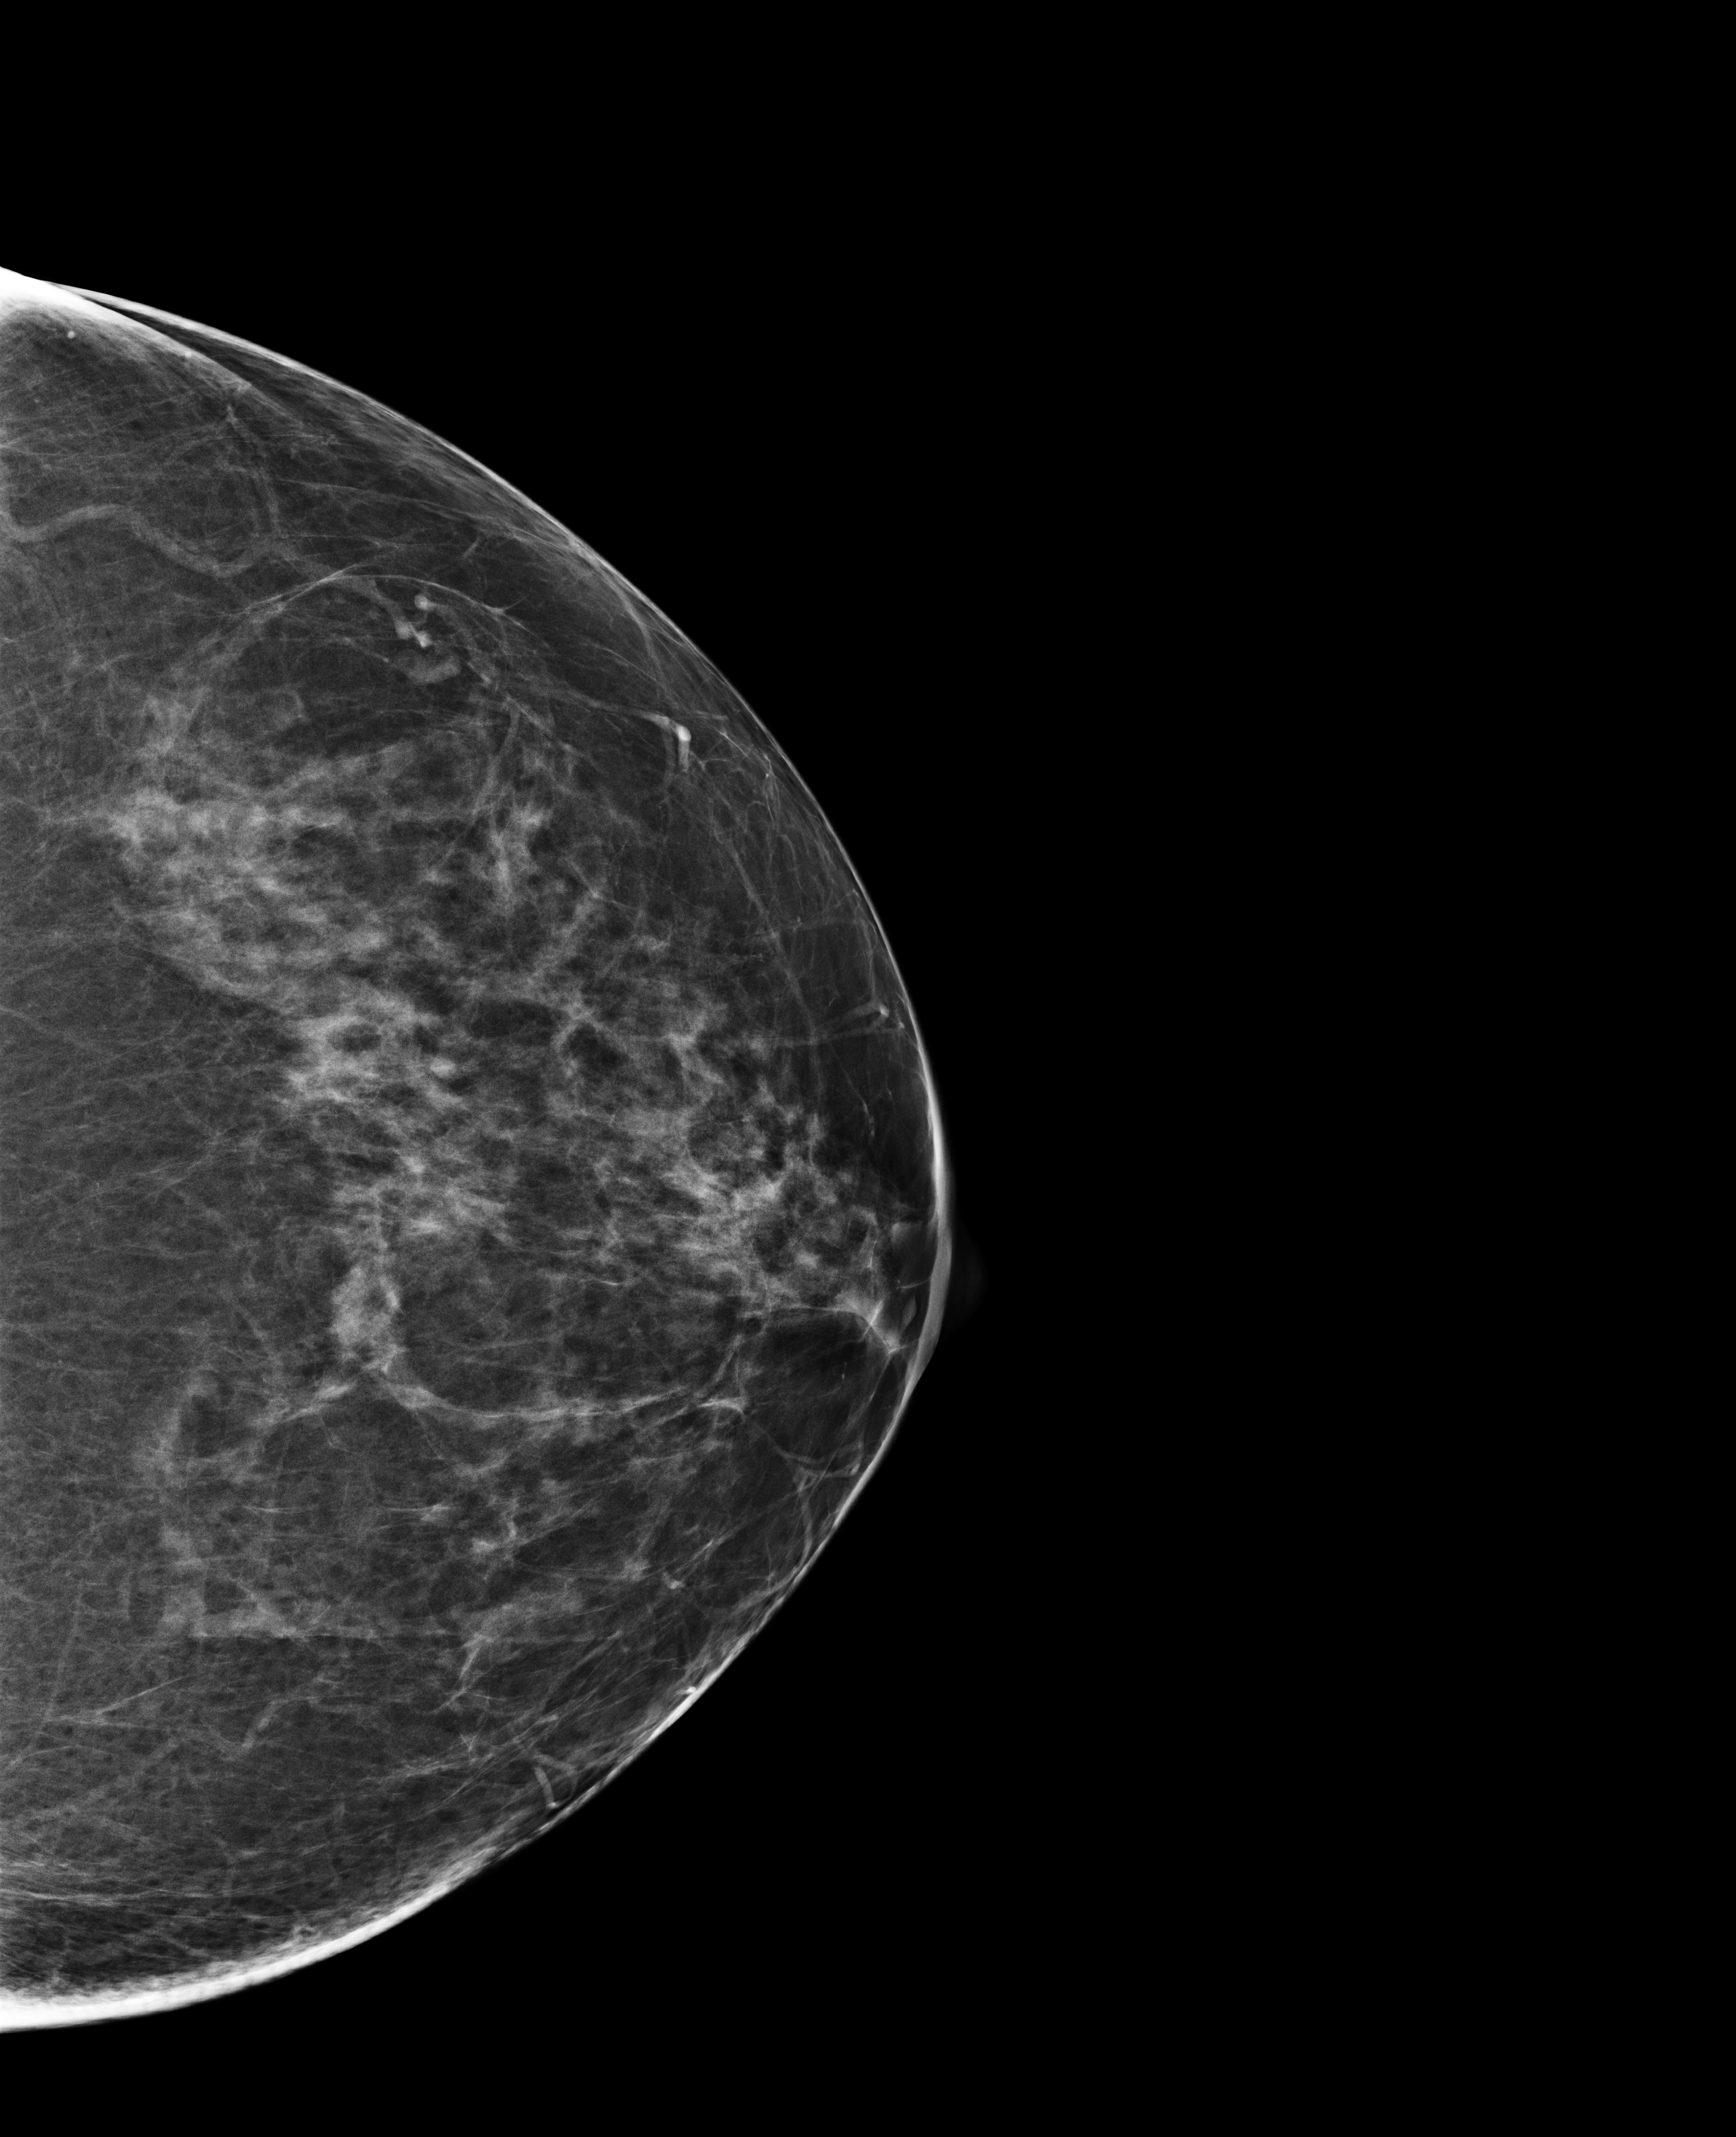
Digital mammogram (FFDM); left breast; craniocaudal (CC) view; annual screening mammography examination; compressed breast thickness 84 mm; system: Selenia Dimensions. Patient: female, 59 years.
BI-RADS breast density category at the screening exam (both breasts, scale 1–4): 3. Final BI-RADS assessment for this screening round (tomosynthesis exam, both breasts): category 1. Recall: no recall after this screen.